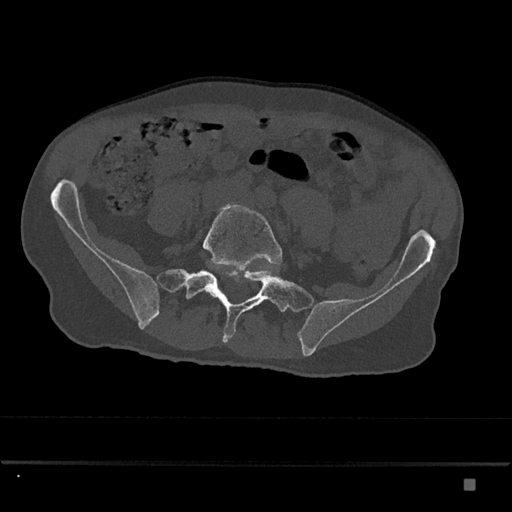
CT including the spine, one axial slice. Slice 252 of 797 in the series (ordered by position). 120 kVp. Bone window (W 1800 / L 400 HU). 0.5 mm slice thickness. 512 × 512 image matrix, field of view 390 × 390 mm. Male patient, age 72 years. Case-level facts recorded for this patient, not image findings: primary cancer: prostate.
Annotated regions visible in this slice (semi-automatically segmented with operator editing):
- L5 vertebra: bounding box [x1, y1, x2, y2] px = [202, 203, 282, 294]